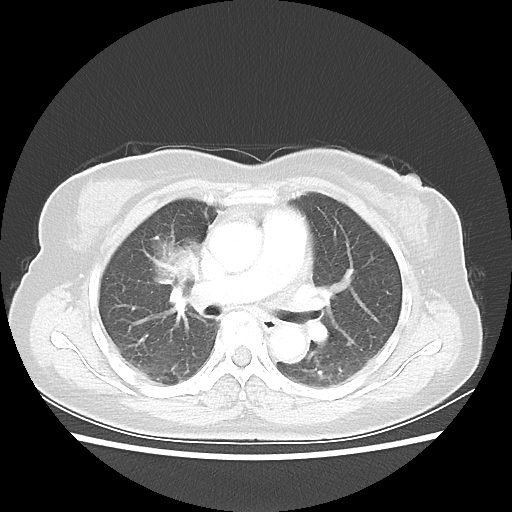
Chest CT, one axial slice. Position 32 of 55 along the scan axis. Lung window (W 1500 / L -600 HU). 5 mm slice thickness. 512 × 512 image matrix, field of view 337 × 337 mm. Female patient, age 62 years. Case-level facts recorded for this patient, not image findings: clinical TNM (as recorded): T4 N3 M0.
Structures marked on this image (bounding box drawn by a radiologist):
- lung tumour (recorded histology: squamous cell carcinoma): box from (x=147, y=227) to (x=209, y=298) px